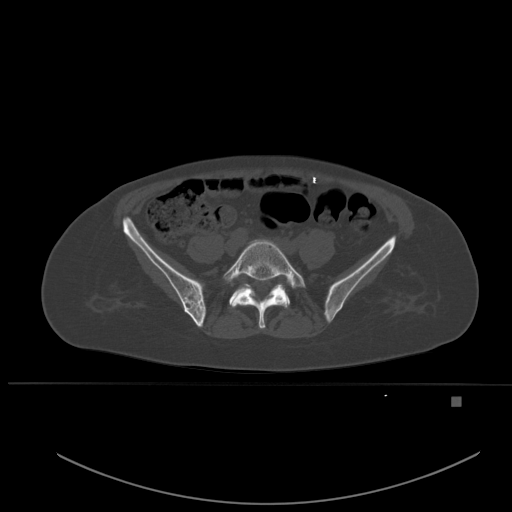
CT including the spine, one axial slice; position 152 of 651 along the scan axis; bone window (W 1800 / L 400 HU); 1.5 mm slice thickness; 512 × 512 image matrix, field of view 443 × 443 mm. Patient: female, 49 years. From the clinical record (not read from this slice): primary cancer: breast.
Outlined on this slice (semi-automatically segmented with operator editing):
- L5 vertebra: bounding box <223,239,305,329> (left, top, right, bottom; pixels)